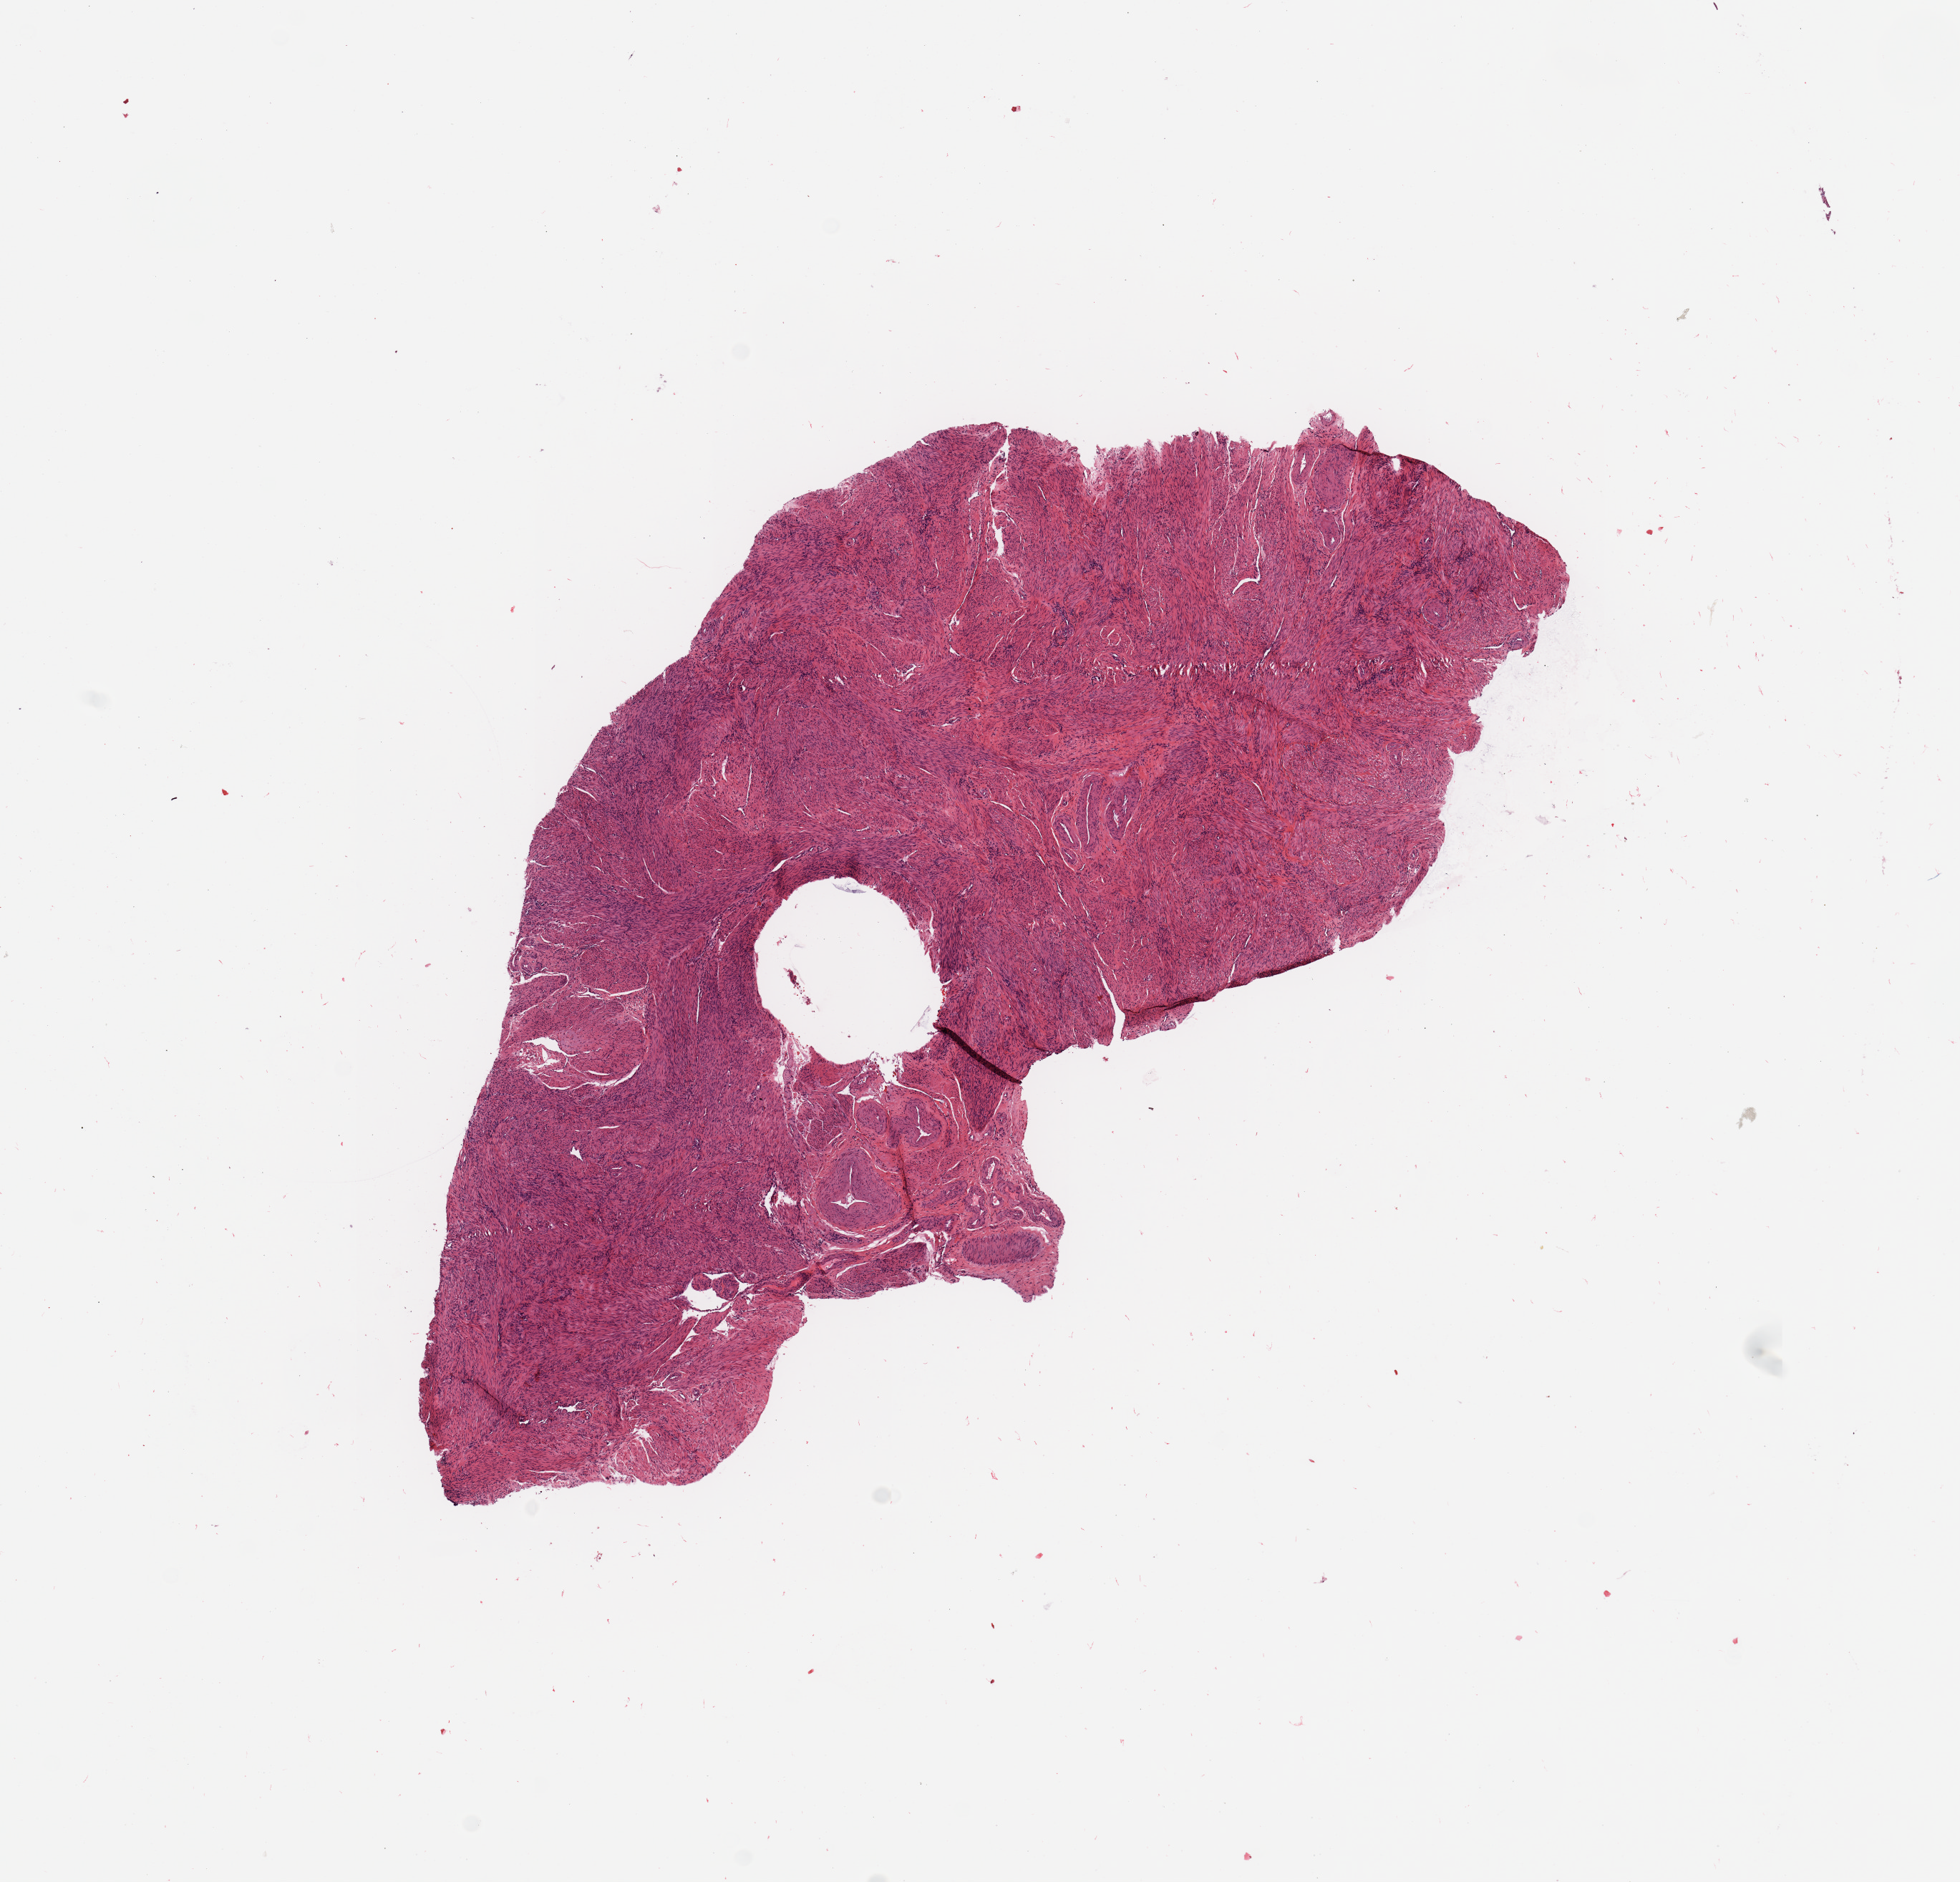
Digitized H&E-stained tissue section (whole slide), whole scanned area (about 10.8 x 10.4 mm) shown as a low-resolution overview; uterus, normal (non-tumour) tissue. 63-year-old female patient.
- this section: normal (non-tumour) tissue from the same patient
- patient diagnosis: Endometrioid adenocarcinoma, NOS